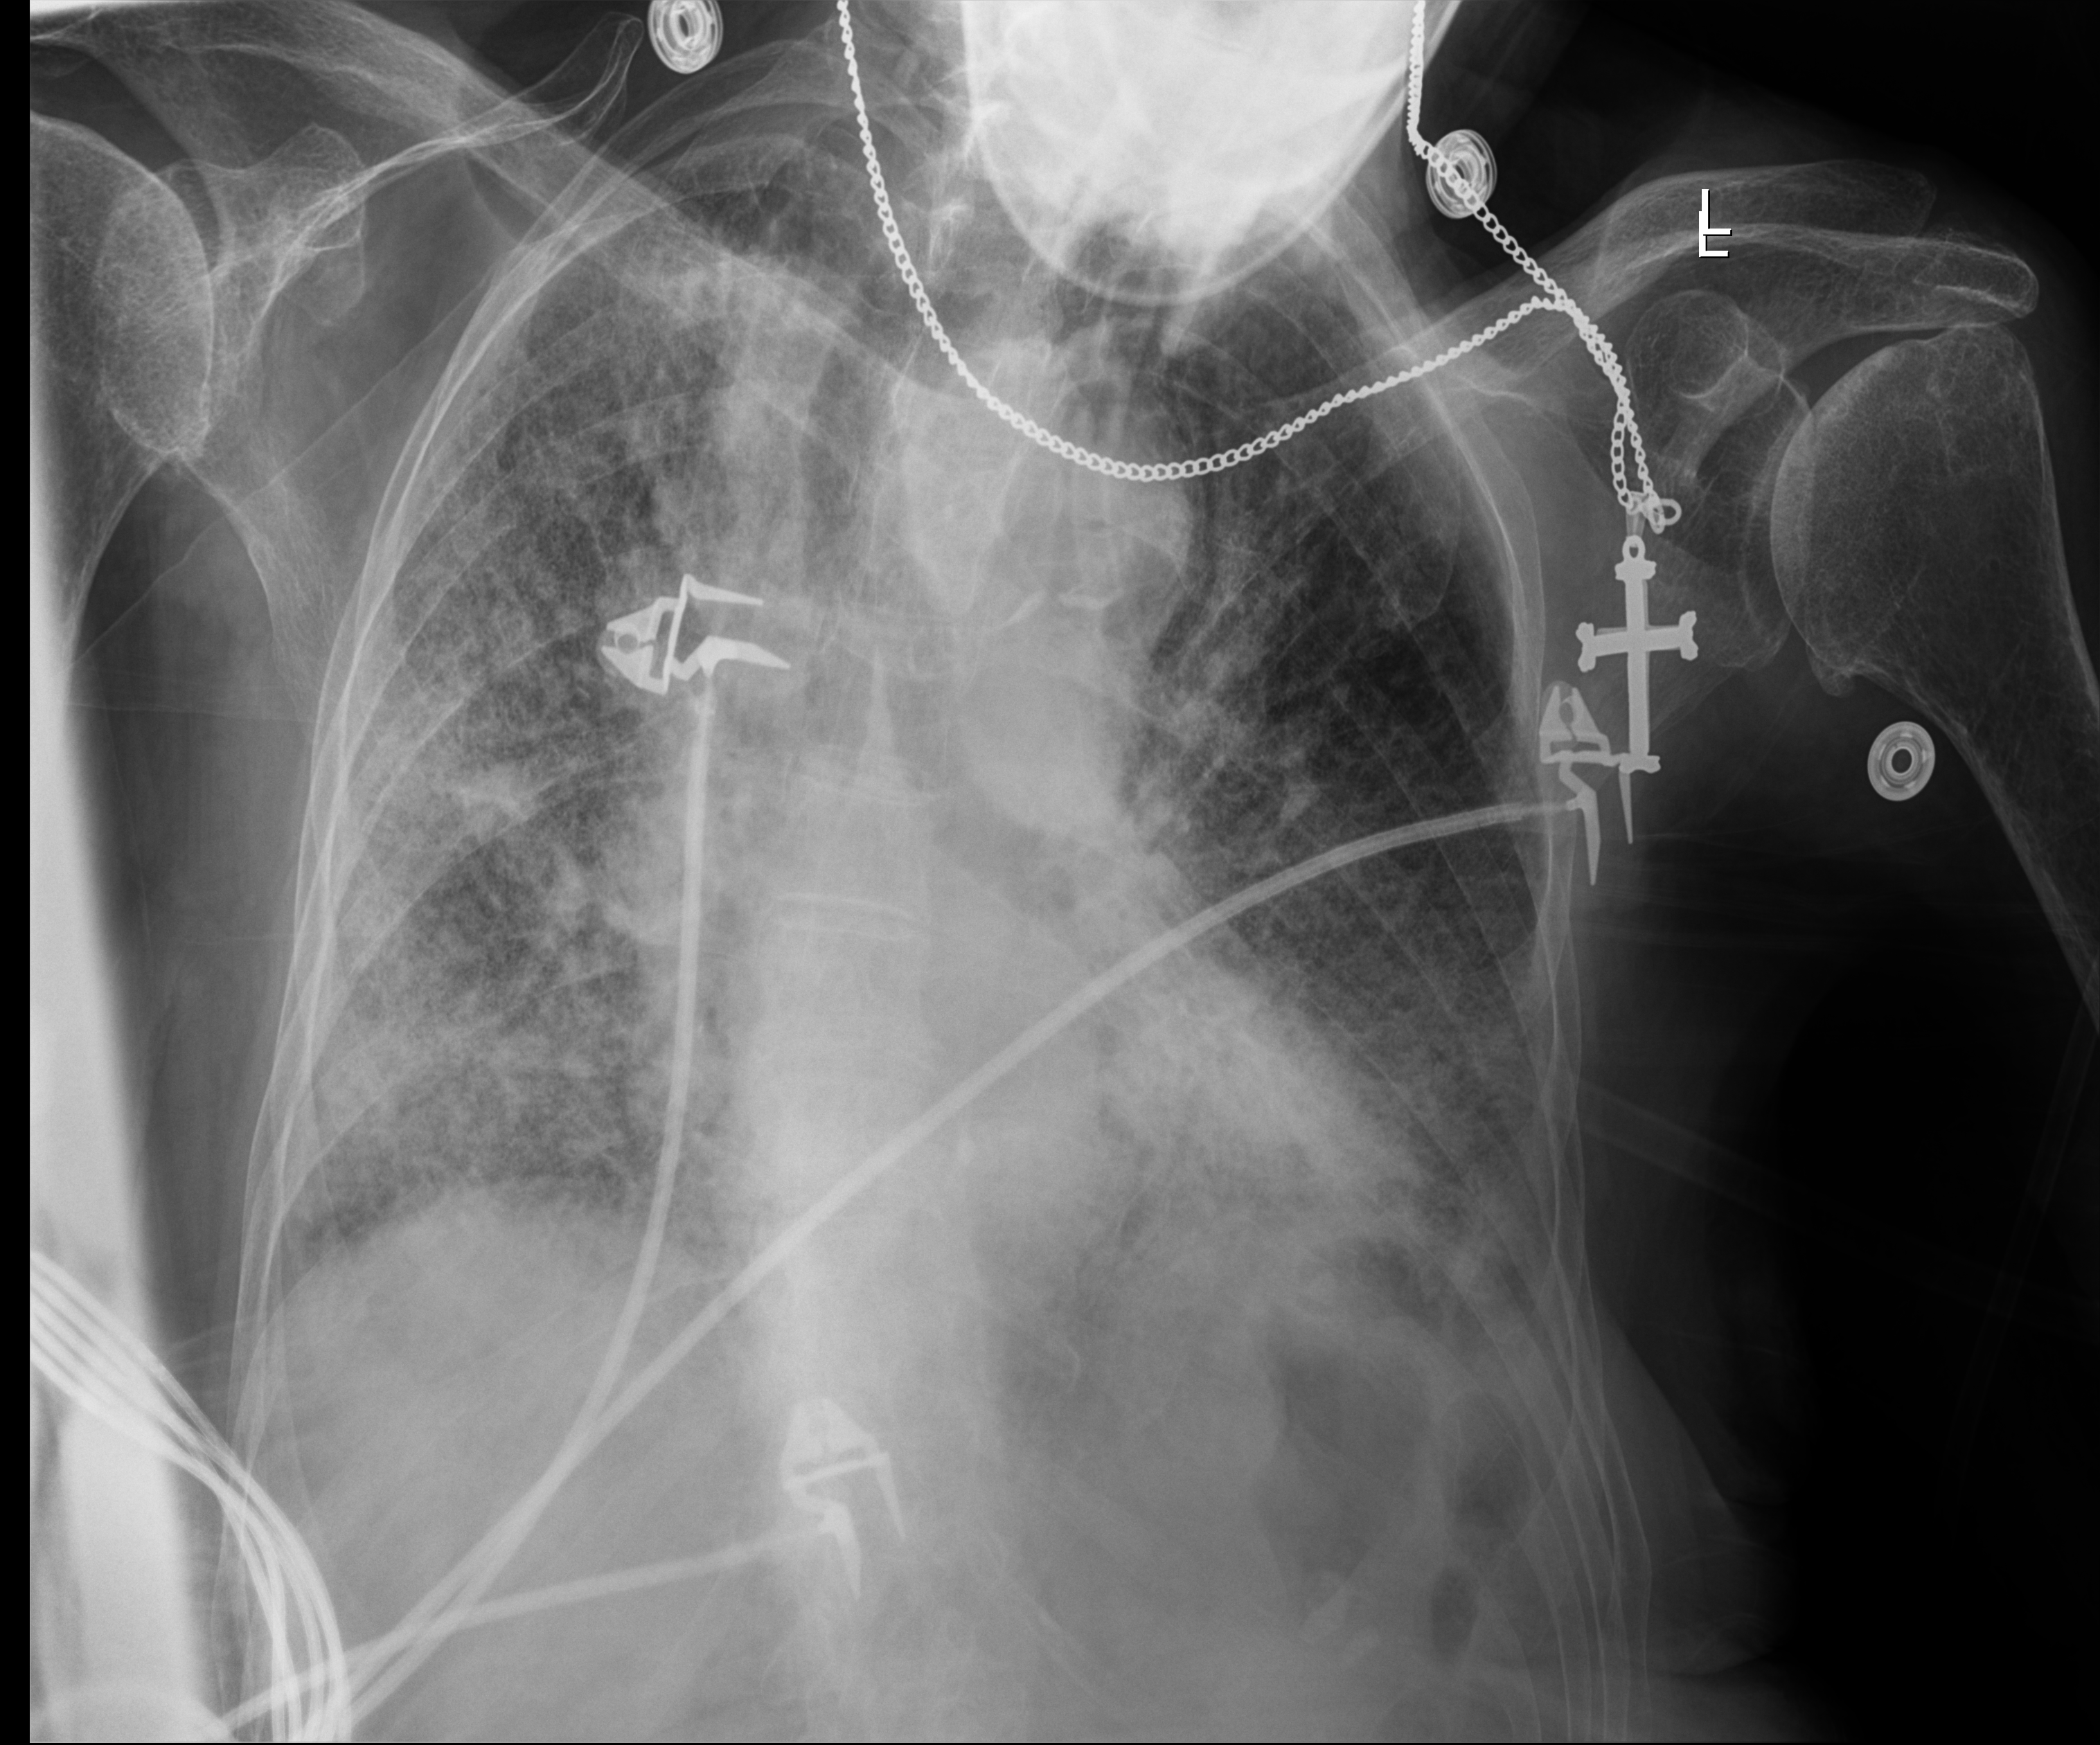
Chest X-ray (portable); anteroposterior (AP) projection. Patient hospitalised with COVID-19; female, aged 75–90 years.
Hospital-stay facts (about this admission, not read from this image; timing relative to this image not recorded):
- admitted to intensive care during this hospital stay: no
- mechanically ventilated during this hospital stay: no